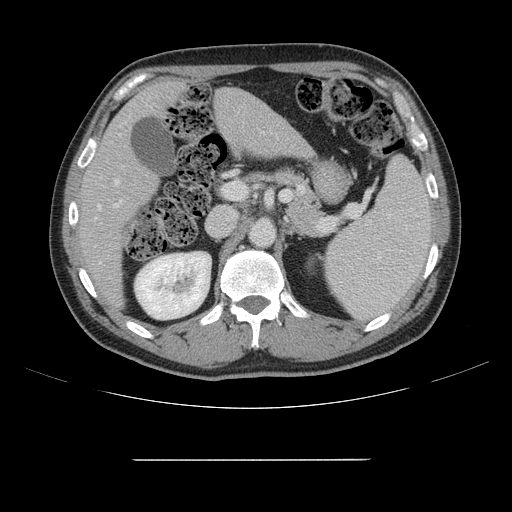
Contrast-enhanced abdominal CT, one axial slice; 120 kVp; intravenous contrast given; soft-tissue window (W 400 / L 40 HU); 512 × 512 image matrix, field of view 404 × 404 mm. Male patient, age 54 years. Case-level facts recorded for this patient, not image findings: diagnosis: colorectal cancer liver metastases, imaged before liver resection; multiple liver metastases: yes; largest metastasis: 1 cm; chemotherapy before resection: yes.
Structures marked on this image (expert manual segmentation):
- hepatic veins: bounding box <98,180,119,264> (left, top, right, bottom; pixels)
- liver: <81,82,308,300>
- planned liver remnant (the part of the liver to remain after resection): <81,82,228,303>
- portal vein (with intrahepatic branches): <114,122,126,208>